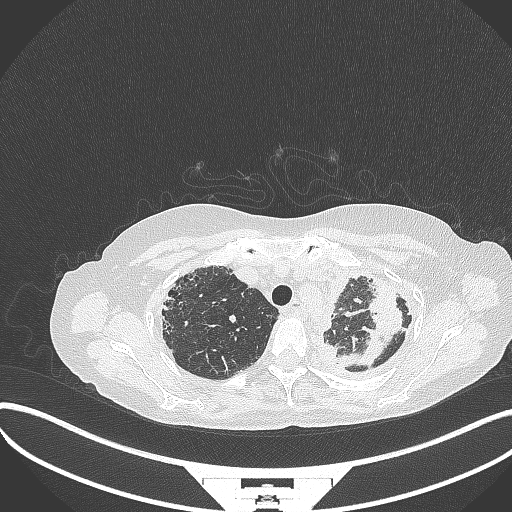
Chest CT, one axial slice; position 278 of 373 along the scan axis; reconstruction kernel B70f; 120 kVp; lung window (W 1500 / L -600 HU); 1 mm slice thickness; 512 × 512 image matrix, field of view 400 × 400 mm. Patient: female, 56 years. From the clinical record (not read from this slice): clinical TNM (as recorded): T1 N0 M0.
Structures marked on this image (rectangle marked by the reading radiologist):
- lung tumour (recorded histology: adenocarcinoma): bounding box [x1, y1, x2, y2] px = [346, 279, 401, 372]